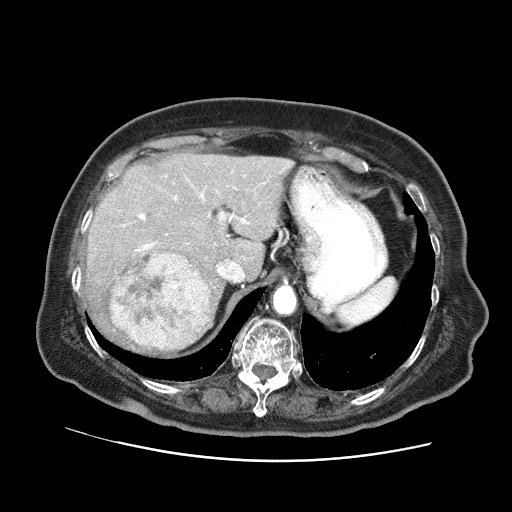
Contrast-enhanced abdominal CT (liver protocol), one axial slice; position 49 of 73 along the scan axis; reconstruction kernel STANDARD; 120 kVp; soft-tissue window (W 400 / L 40 HU); 2.5 mm slice thickness; 512 × 512 image matrix, field of view 380 × 380 mm. Case-level facts recorded for this patient, not image findings: diagnosis: hepatocellular carcinoma (patient treated with transarterial chemoembolisation; whether this scan precedes or follows treatment is not stated here); TNM stage (as recorded): Stage-I; Child-Pugh class: A; tumour nodularity: uninodular.
Annotated regions visible in this slice (semi-automatically segmented with operator editing):
- liver parenchyma outside the tumour (the mass and vessels are separate outlines, so this box may not span the whole liver): bounding box (x1, y1, x2, y2) in pixels: (86, 152, 293, 353)
- mass: (108, 253, 209, 350)
- liver vessels: (122, 182, 265, 252)